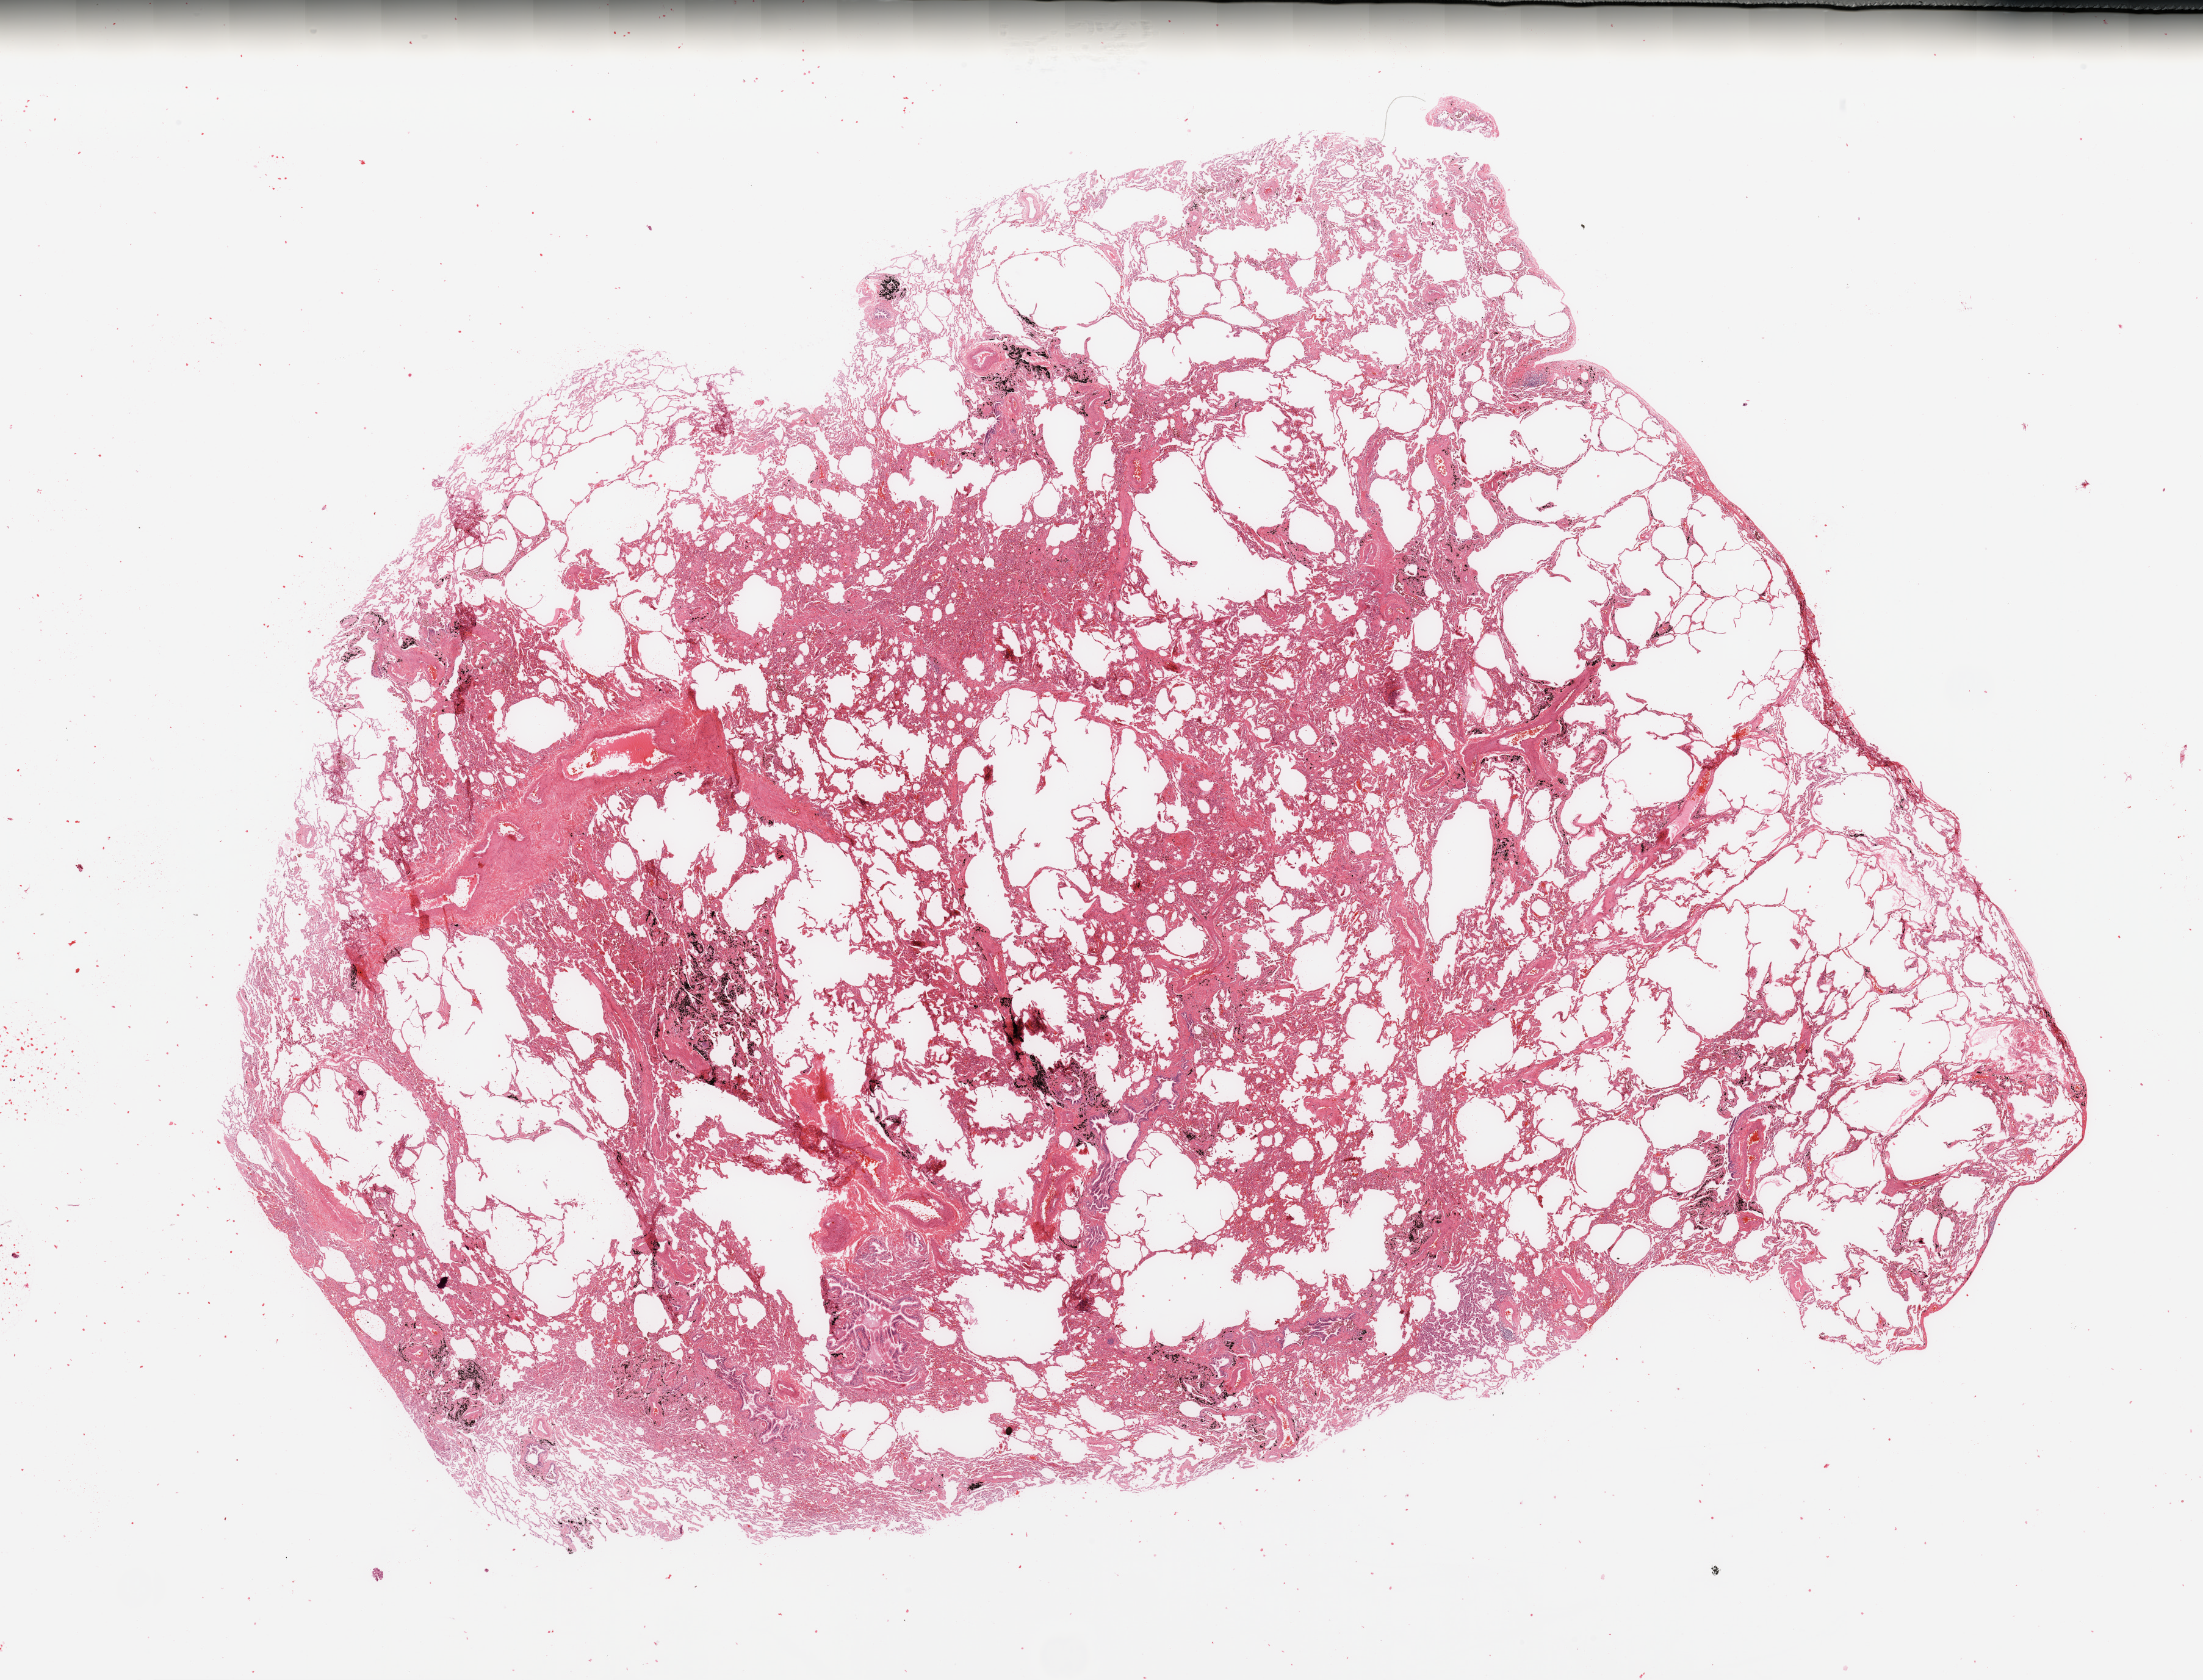
Whole-slide histology image, H&E — a low-resolution overview of the entire scanned area, about 28.5 x 21.8 mm (slide scanned at 20x); normal (non-tumour) tissue sample, sampled site: lung. Male, 56 y/o.
This section: normal (non-tumour) tissue from the same patient. Patient diagnosis: Adenocarcinoma, NOS.